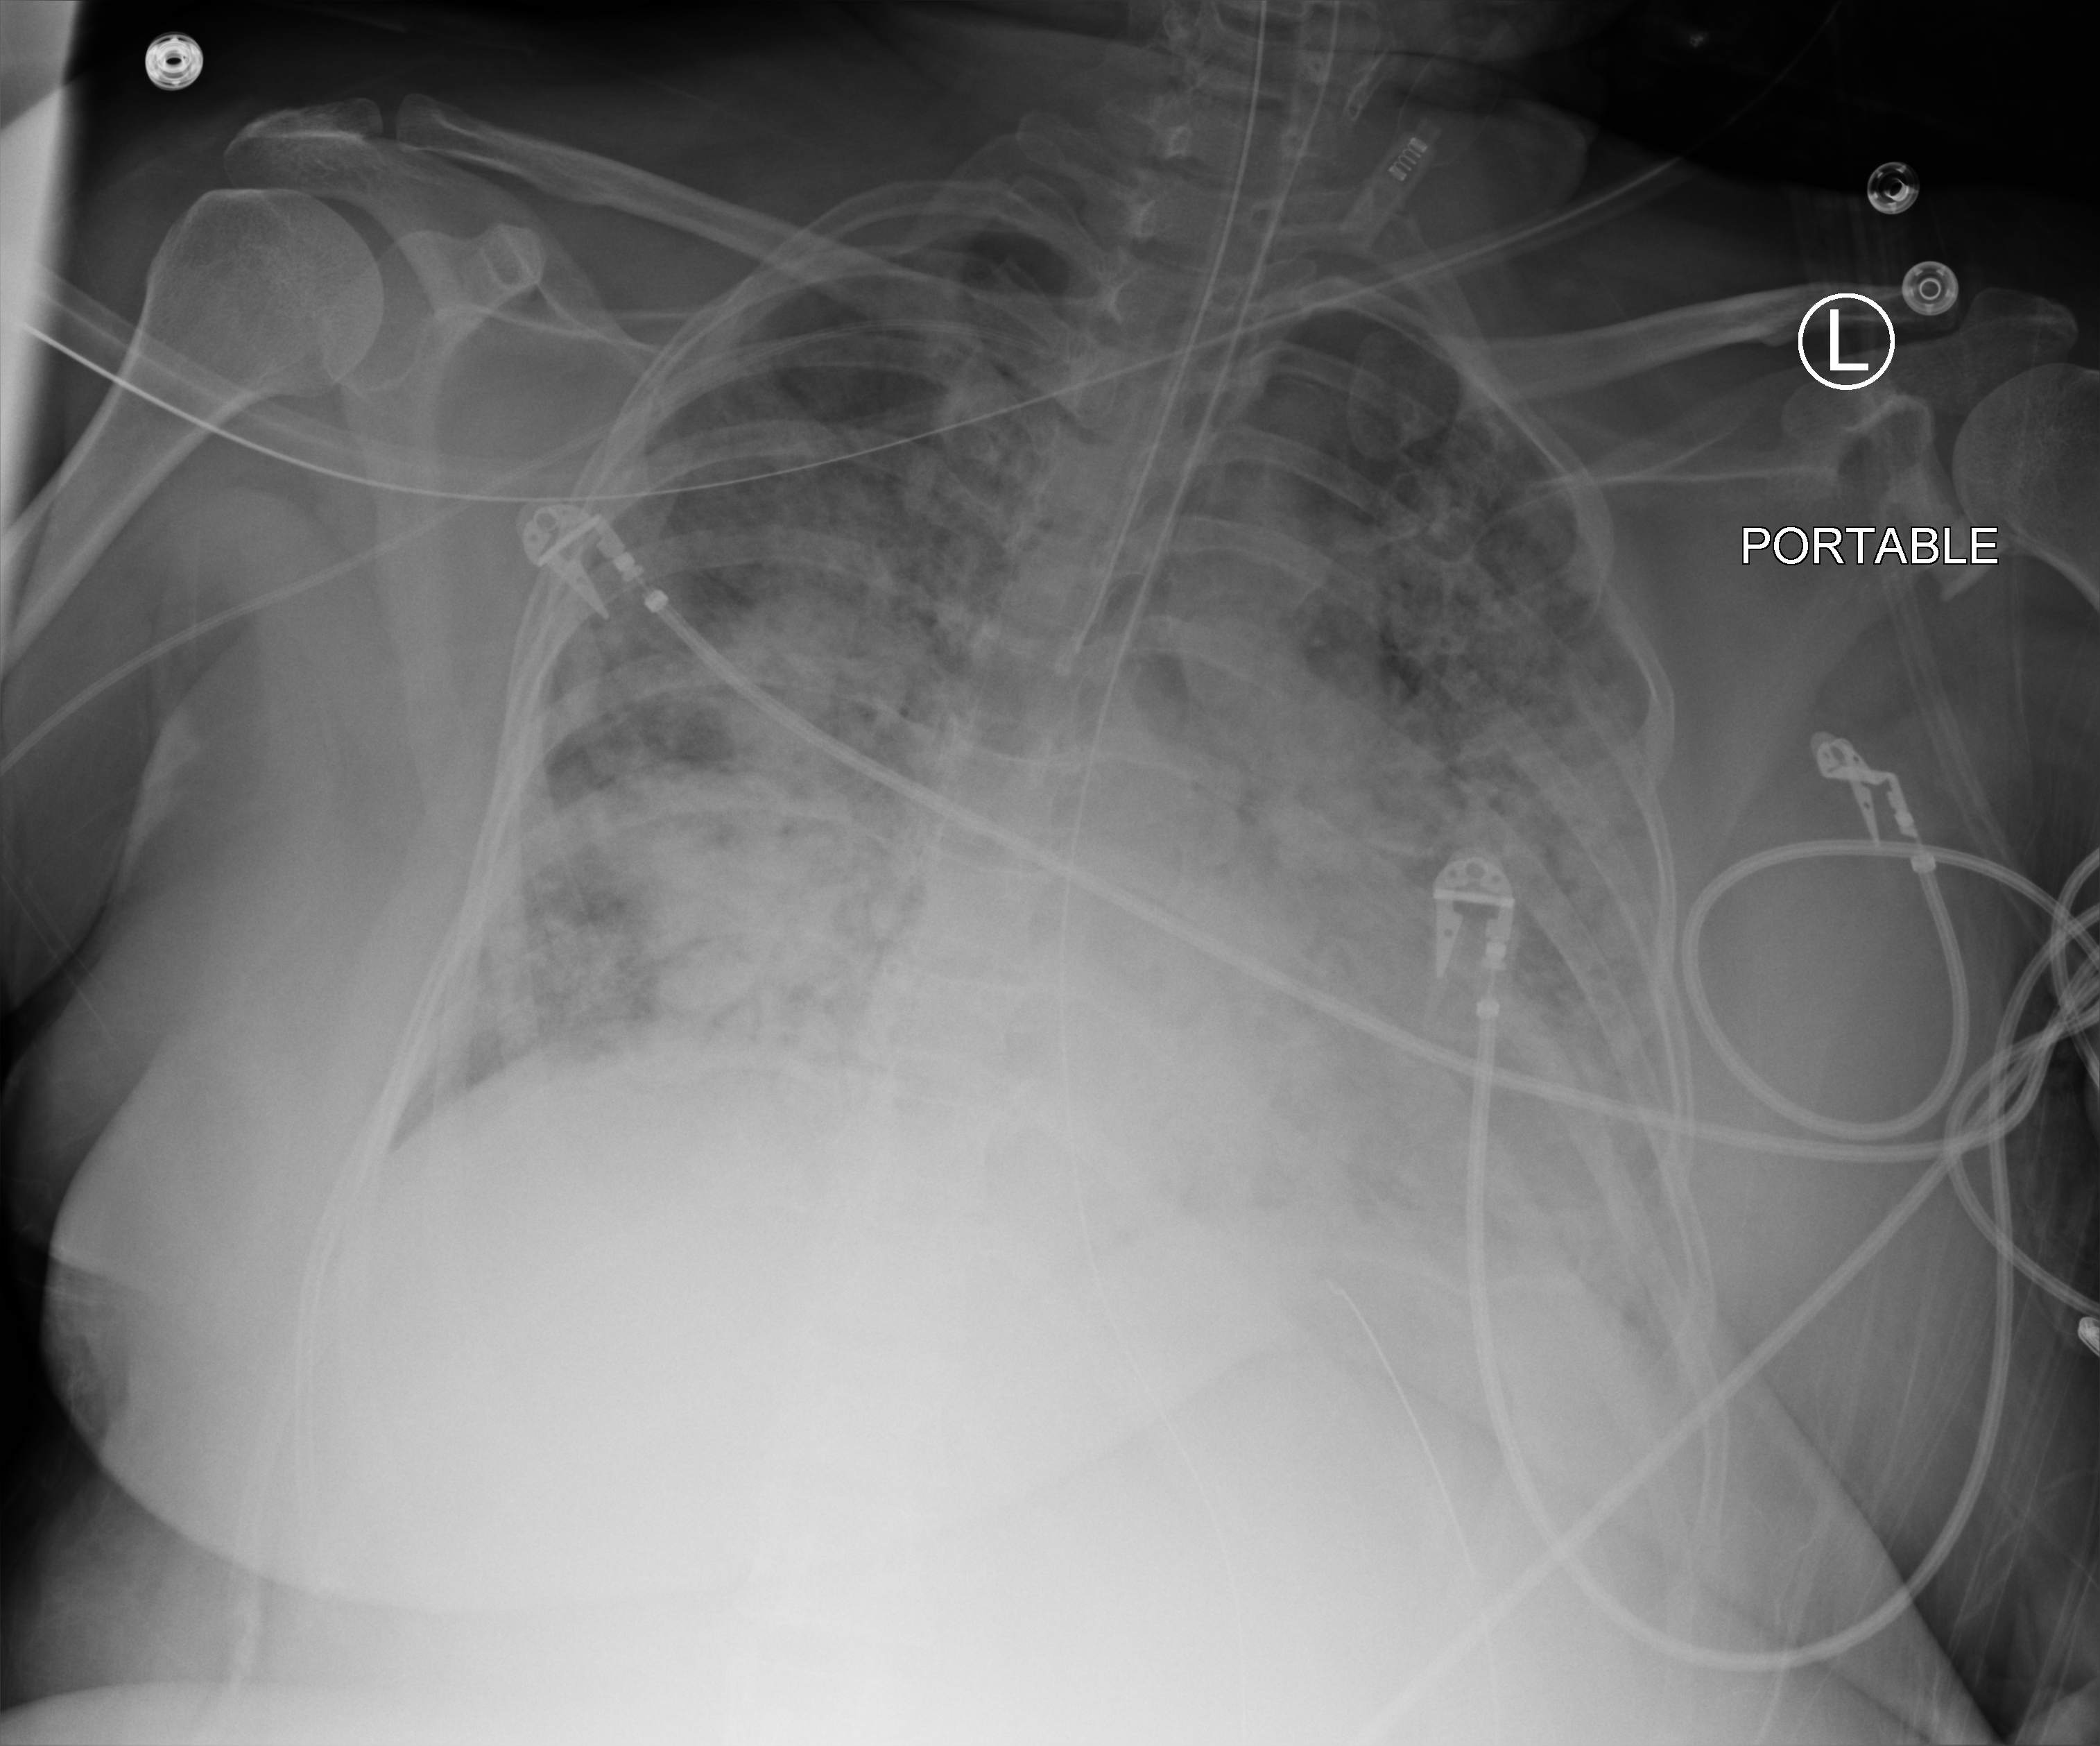
Portable chest radiograph, anteroposterior (AP) projection. Adult patient hospitalised with COVID-19, age 18–59 years.
From the hospital-stay record, not from the radiograph (when in the stay this image was taken is not recorded): admitted to intensive care during this hospital stay: yes; chronic kidney disease (admission record): no; mechanically ventilated during this hospital stay: yes.